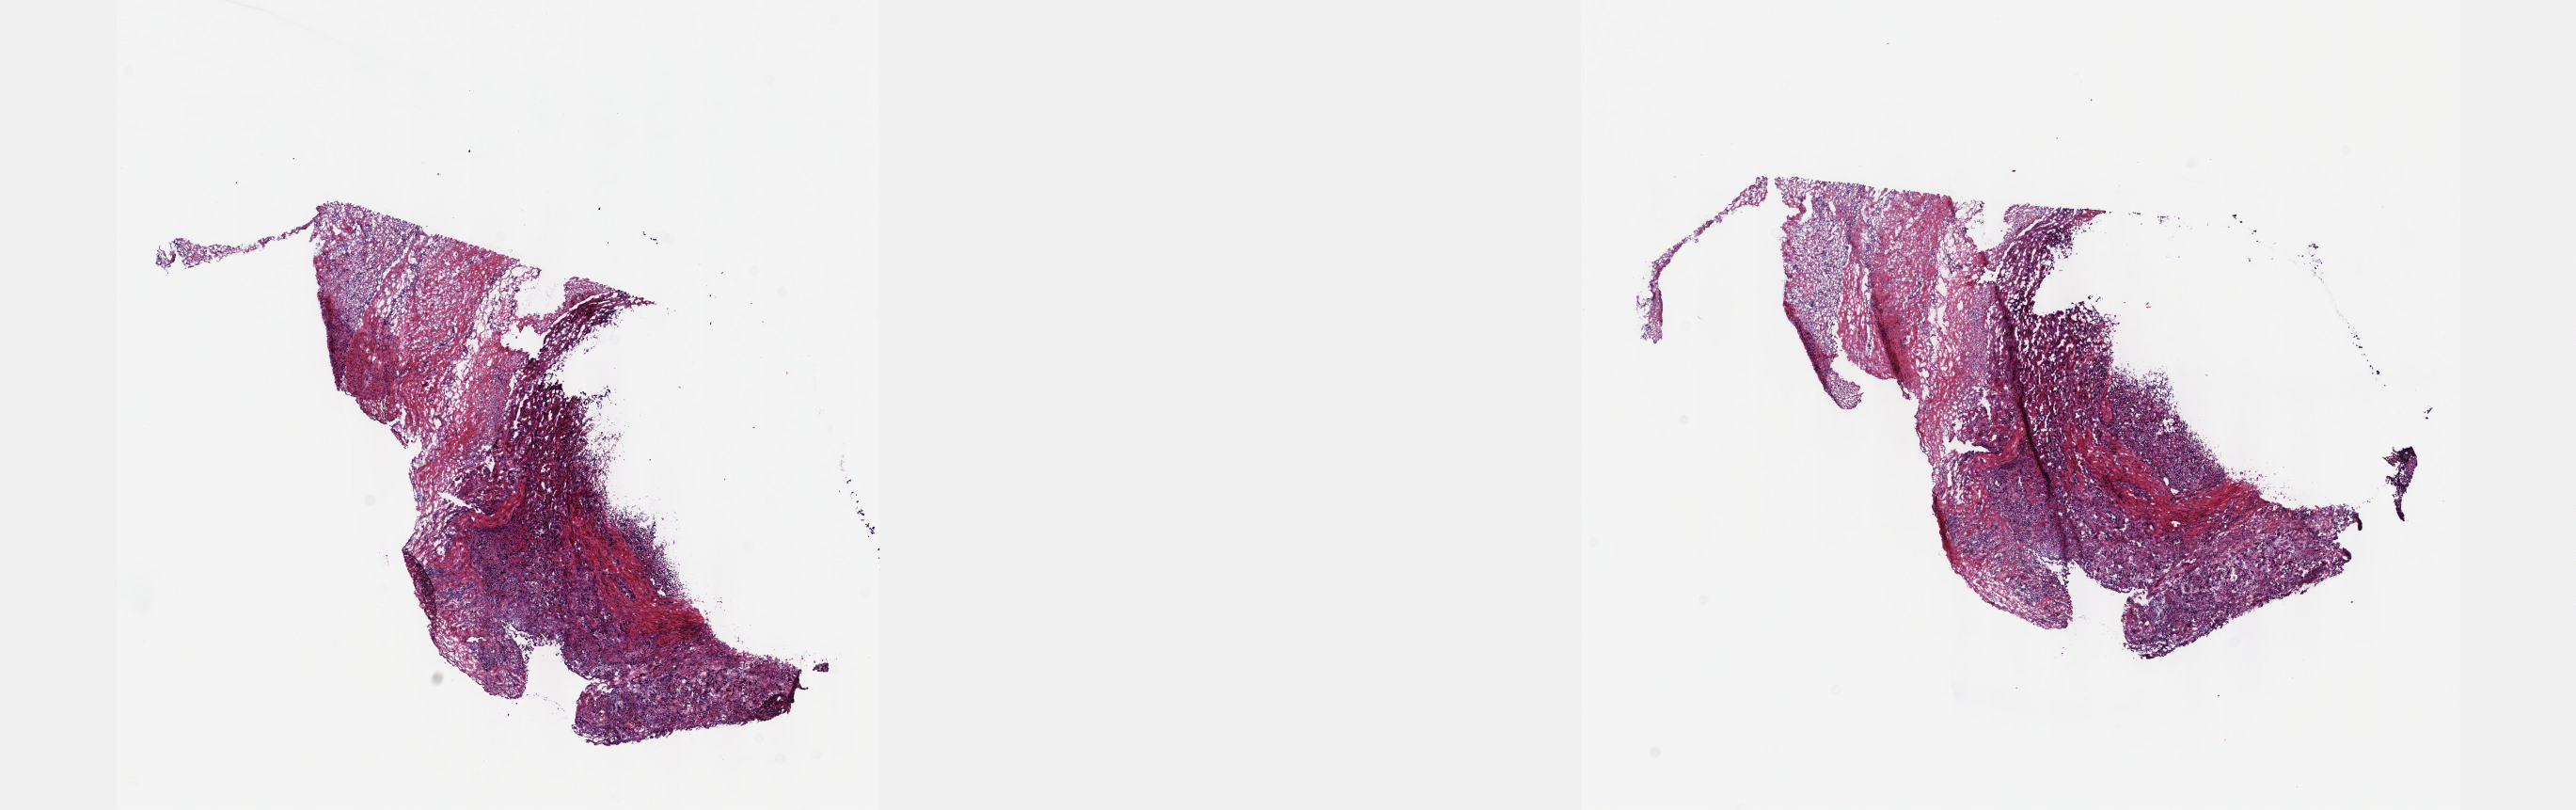
Hematoxylin and eosin (H&E) stained whole-slide image, a low-resolution overview of the entire scanned area, about 22.1 x 7.0 mm, frozen section from the top of the tissue portion, mesothelium, primary tumour sample. Male patient; age at initial diagnosis 54 years. Slide review estimates, as recorded: tumour cells 65%, tumour nuclei 65%, normal cells 0%, stromal cells 35%, necrosis 0%. Inflammatory infiltration, as recorded: lymphocyte infiltration 4%, monocyte infiltration 2%, neutrophil infiltration 6%.
AJCC pathologic stage: IV (7th edition). Laterality: left. Diagnosis: Epithelioid mesothelioma, malignant.